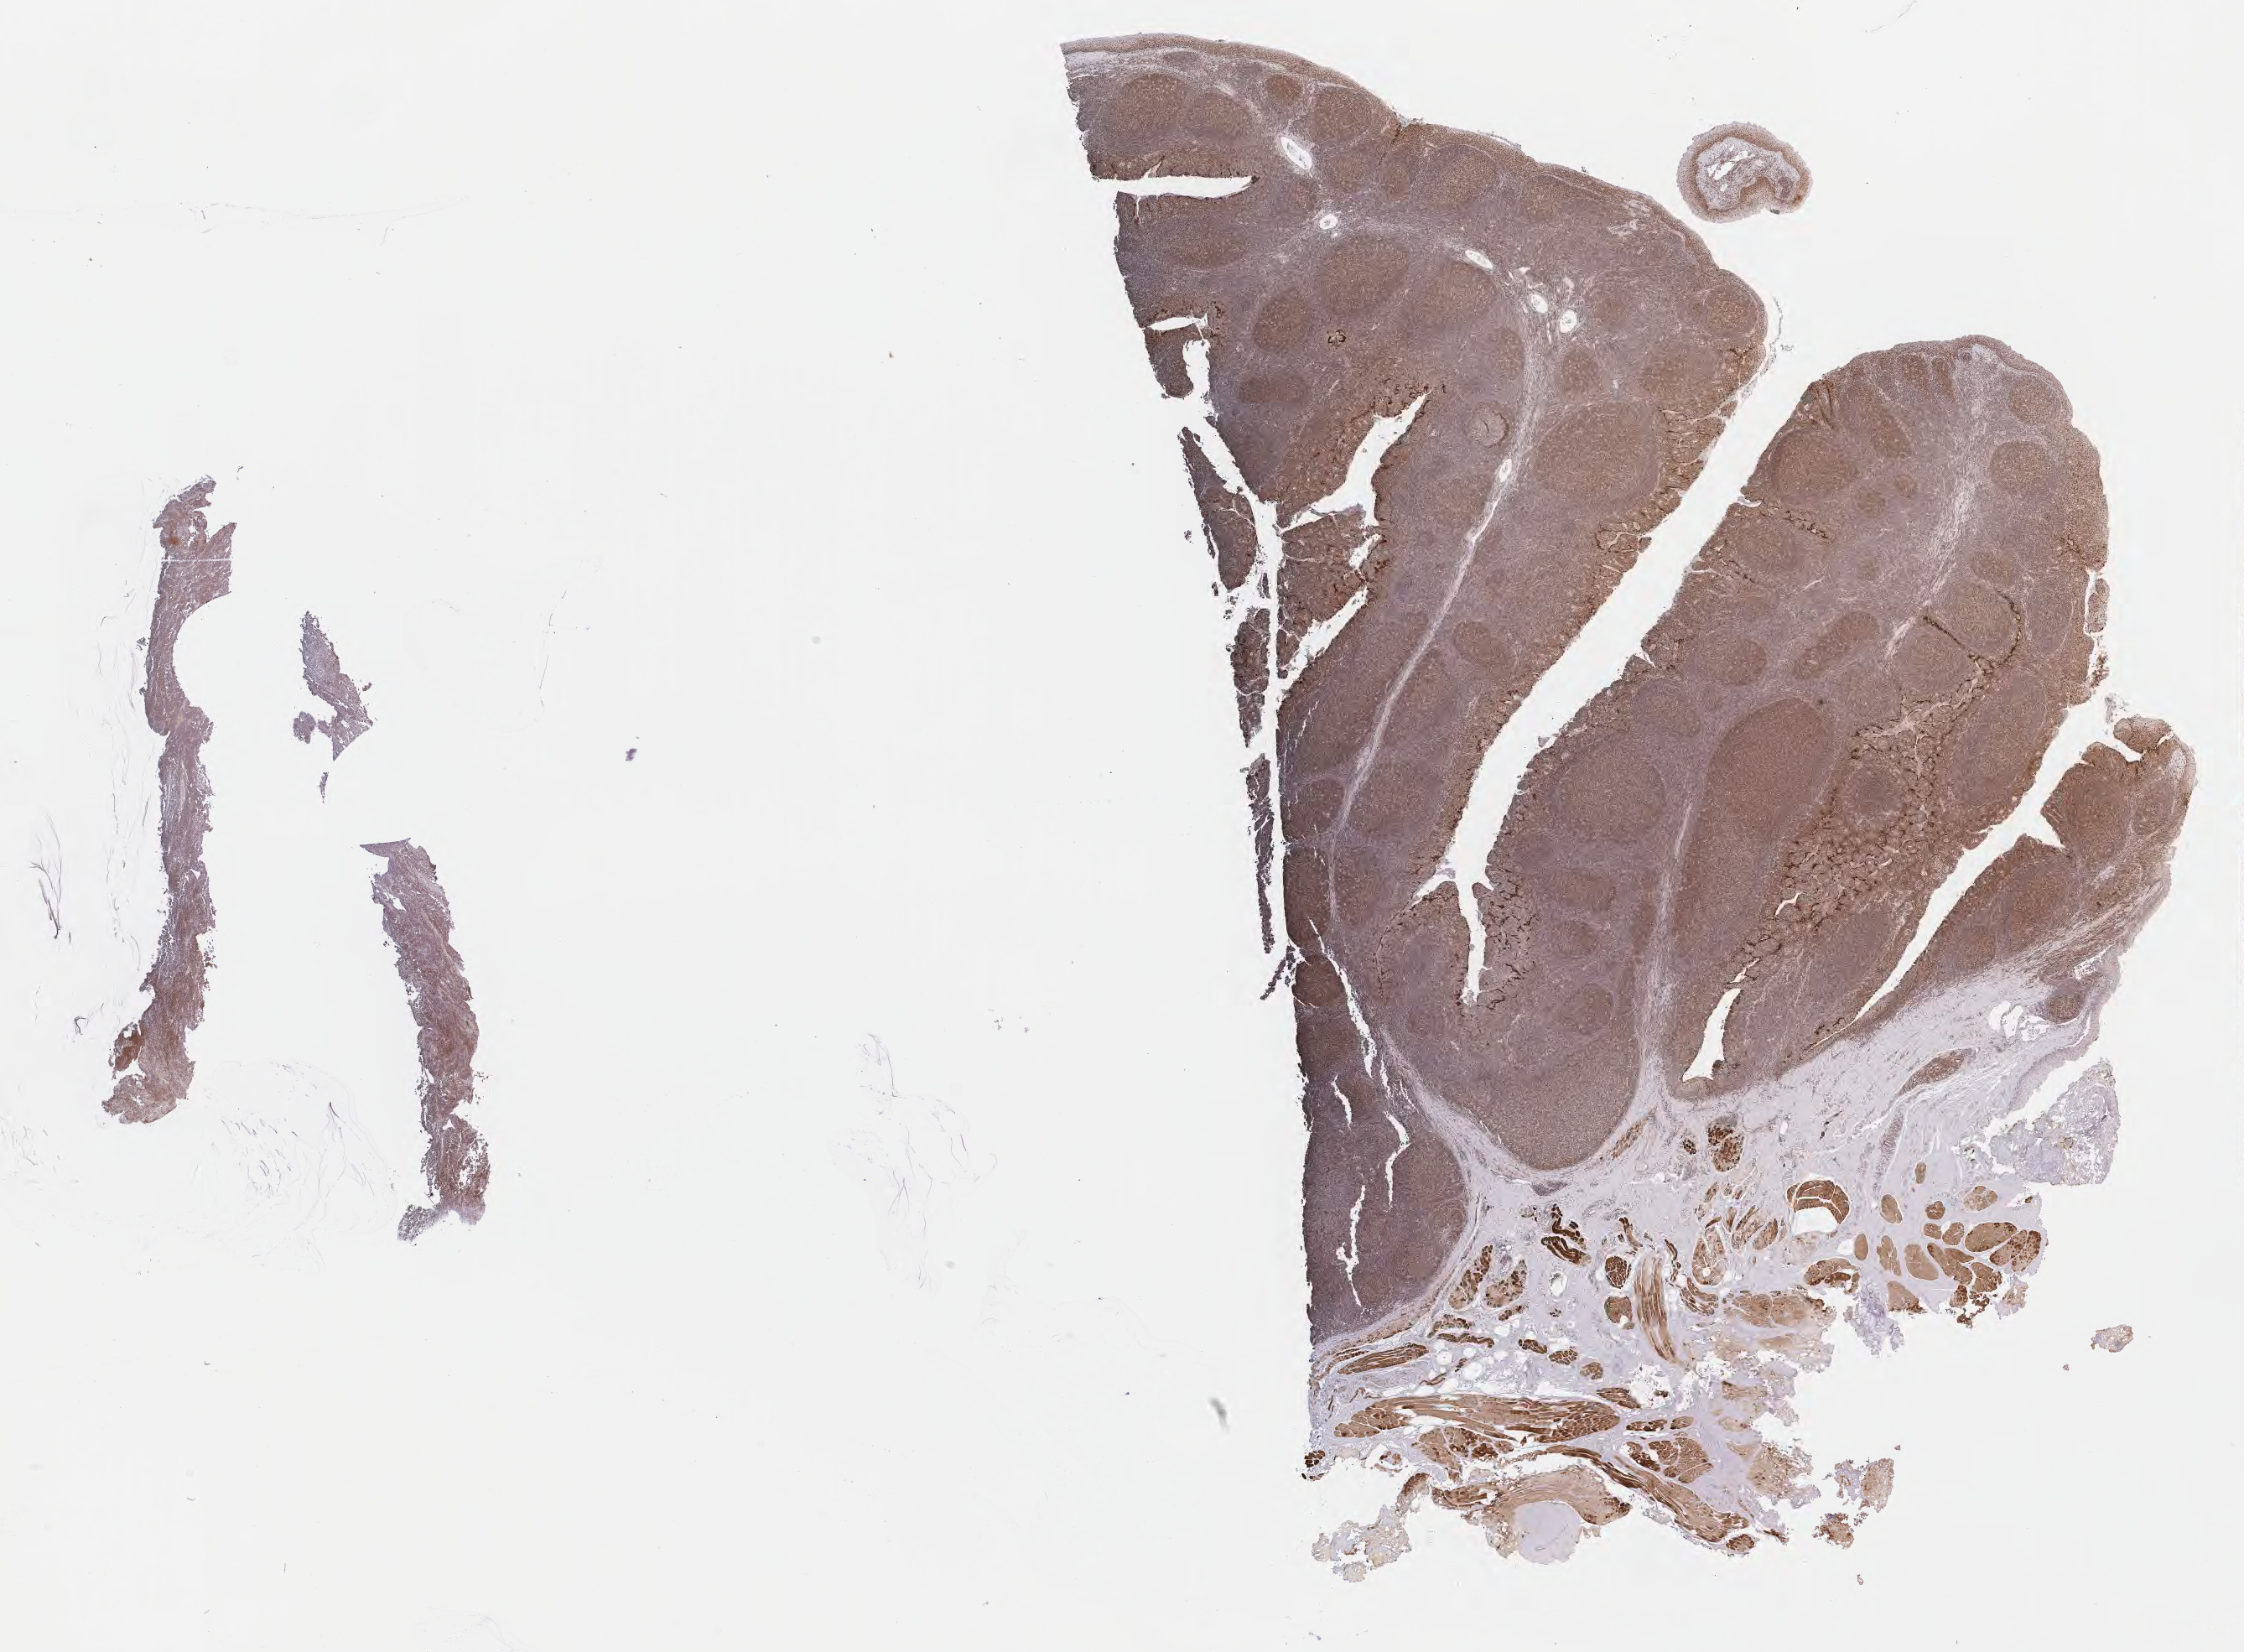
Immunohistochemistry (IHC) whole-slide image stained for BCL6, a low-resolution overview of the entire scanned area, about 21.6 x 15.9 mm; tumor tissue; anatomic site: spleen. Male patient; age at initial diagnosis 6 years.
Diagnosis: Burkitt lymphoma, NOS.